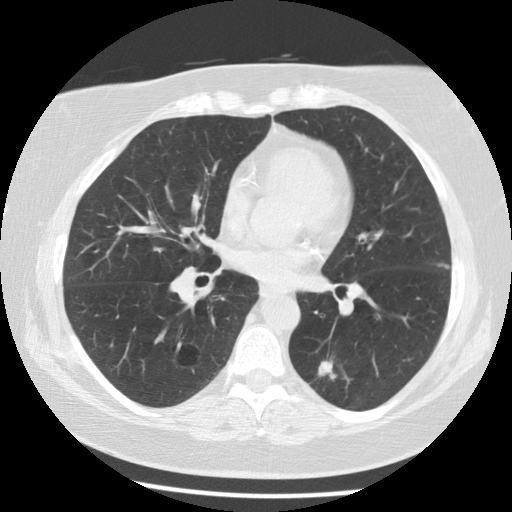
Axial slice from a low-dose chest CT screening exam, third annual screen, lung window (W 1500 / L -600 HU), 2.5 mm slice thickness. Female participant, aged 59 years at enrolment. Current smoker at enrolment.
• Expert reader's lesion annotation, box from (x=289, y=347) to (x=357, y=405) px.
• The screening reader recorded 6 non-calcified nodules or masses ≥4 mm on this exam (right lower lobe, right upper lobe, right lower lobe, right lower lobe, left lower lobe, left lower lobe); which of them this box marks is not recorded.
• Official screen result: positive, other.
• Participant outcome: lung cancer diagnosed 56 days after this screen — adenocarcinoma, NOS, left lower lobe, poorly differentiated (G3), stage IA (AJCC 6th edition), 15 mm at pathology.